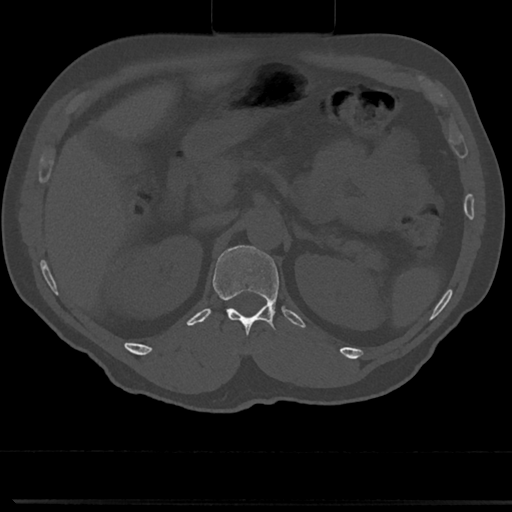
CT including the spine, one axial slice. Slice 138 of 817 in the series (ordered by position). 120 kVp. Bone window (W 1800 / L 400 HU). 512 × 512 image matrix. Male patient, age 61 years. From the clinical record (not read from this slice): primary cancer: prostate.
Annotated regions visible in this slice (semi-automatically segmented with operator editing):
- T12 vertebra: box from (x=212, y=254) to (x=282, y=356) px